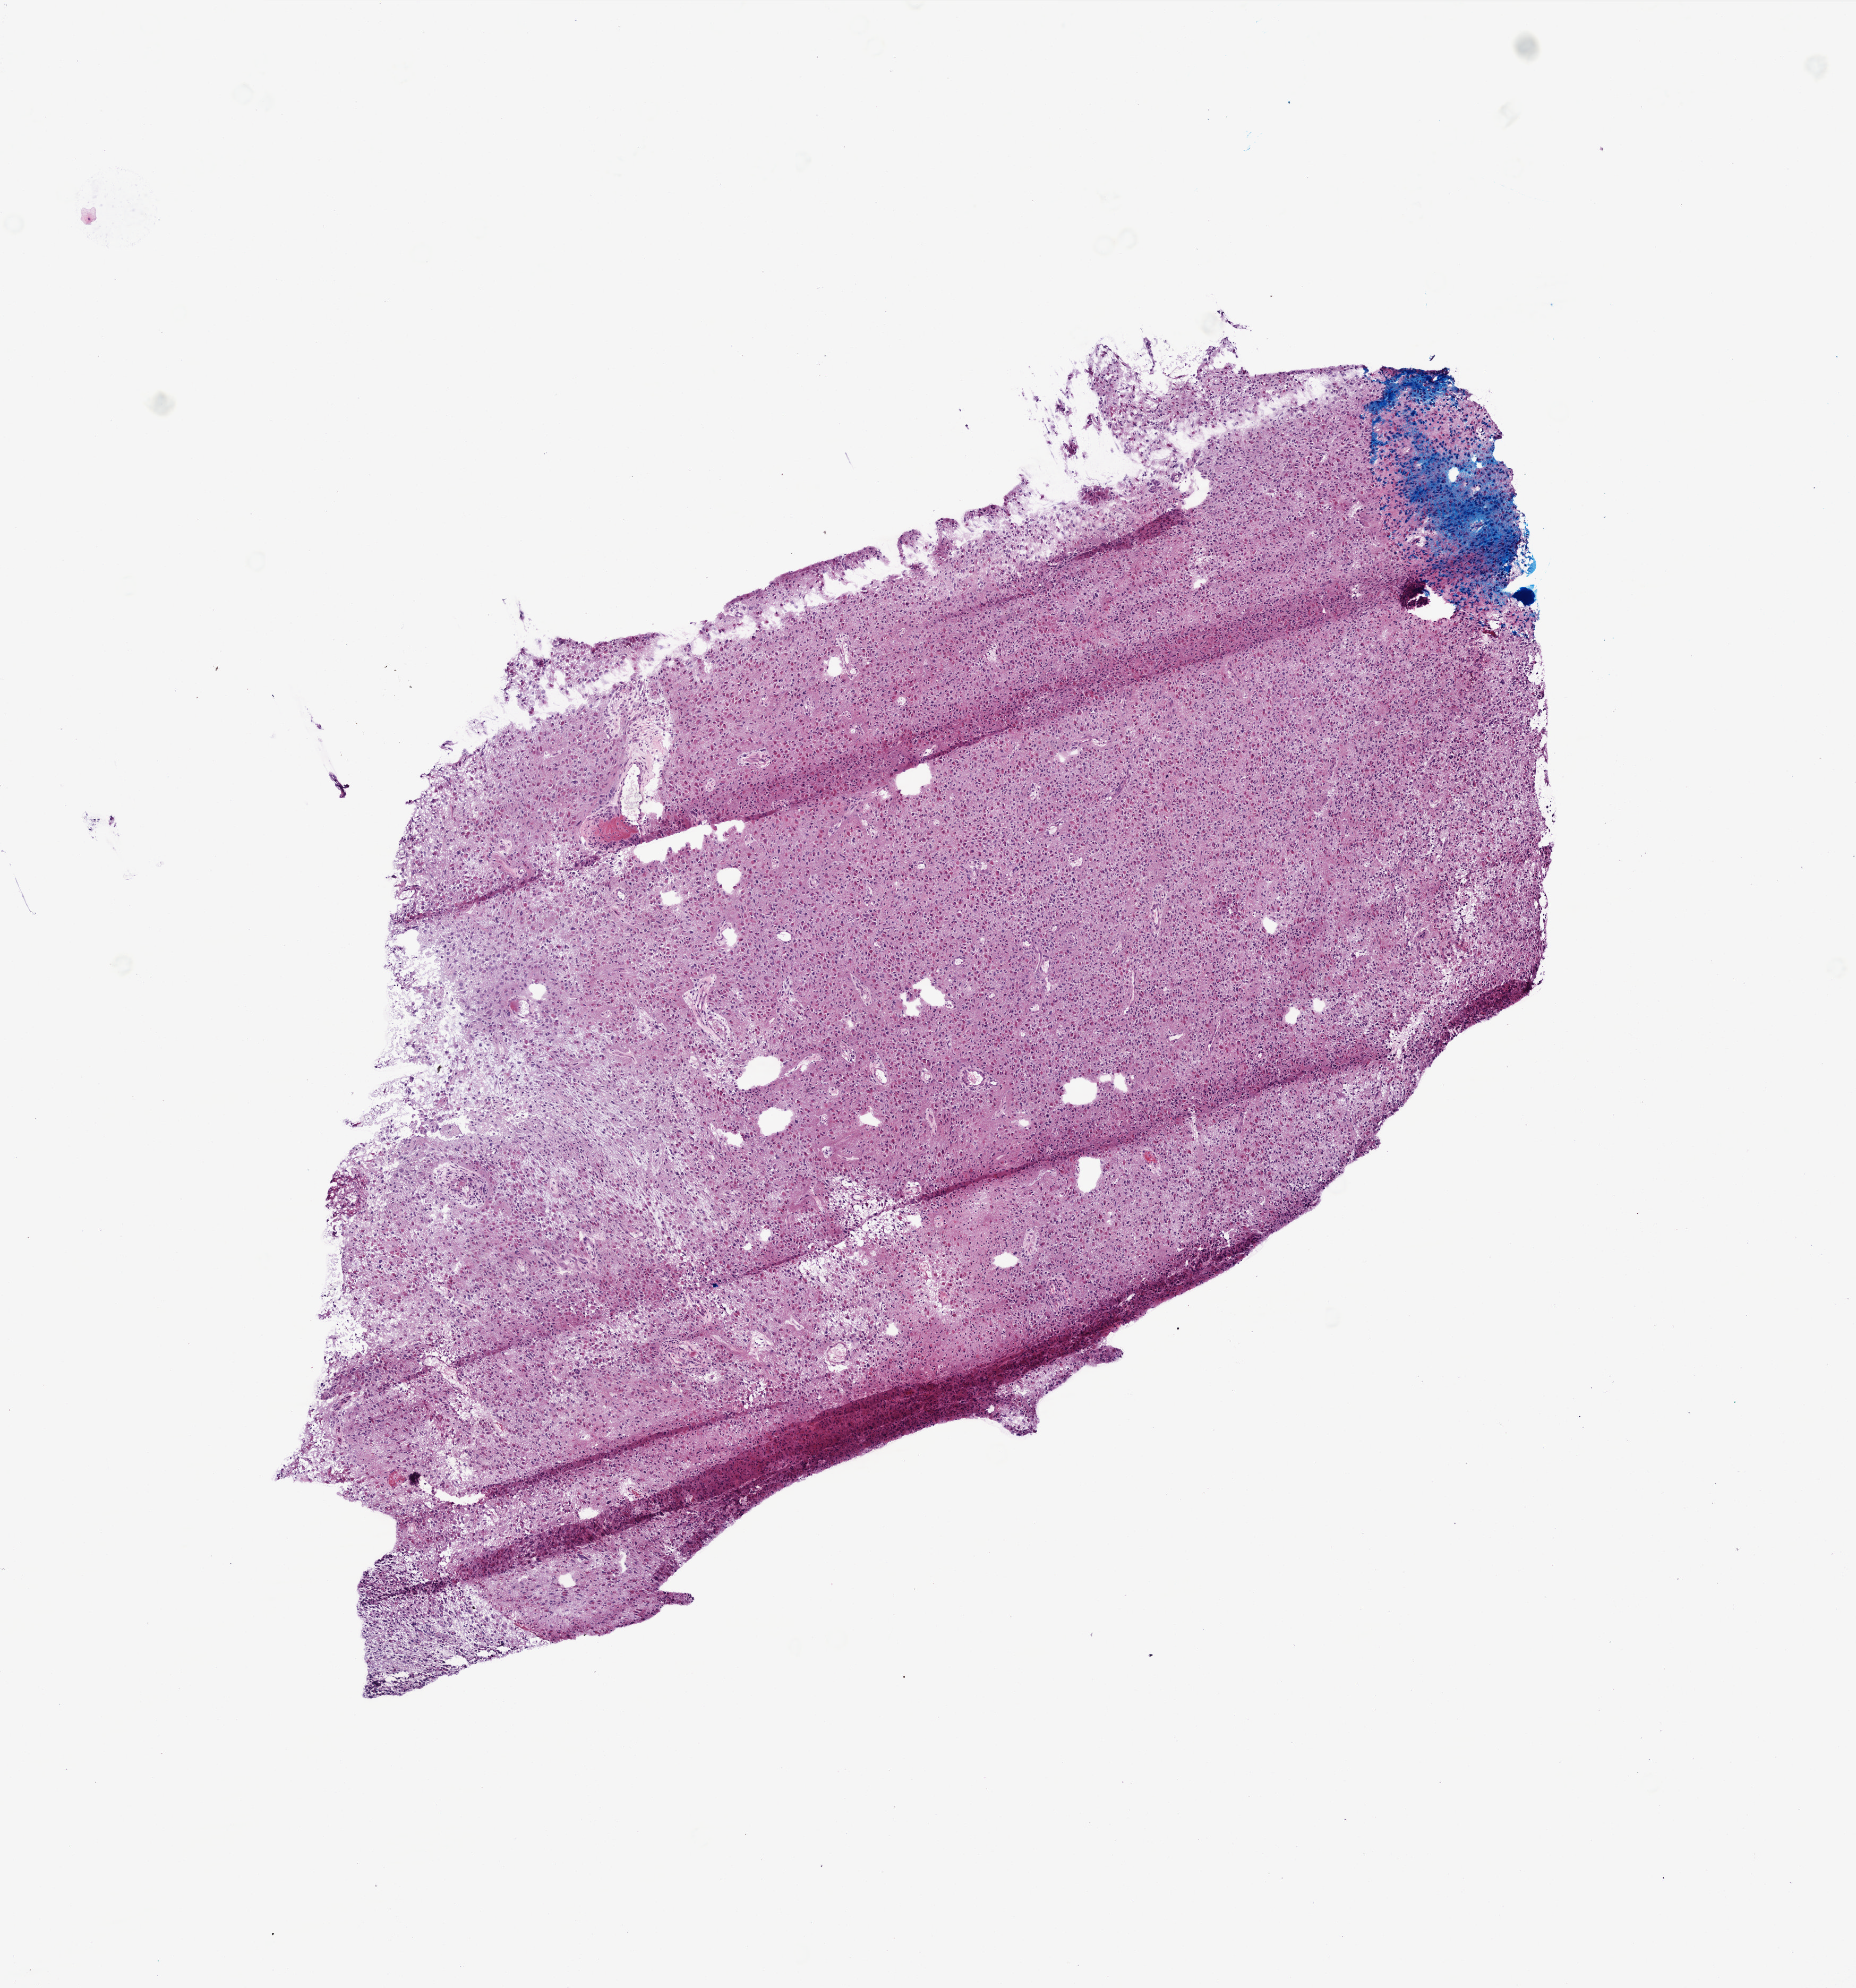
Digitized H&E tissue section (whole slide) — shown as a low-resolution overview of the whole scanned area (about 7.0 x 7.5 mm). Frozen section. Brain, primary tumour sample. Patient: female, age at initial diagnosis 72 years. Pathologist review of this section (percent, as recorded): tumour cells 100%, tumour nuclei 95%, normal cells 0%, stromal cells 0%, necrosis 0%.
Diagnosis: Glioblastoma.